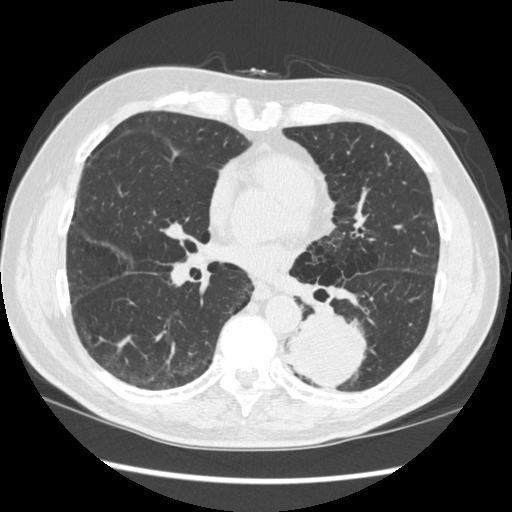
Low-dose screening chest CT, one axial slice; position 153 of 348 along the scan axis; reconstruction kernel STANDARD; 120 kVp; lung window (W 1500 / L -600 HU); 1.25 mm slice thickness; 512 × 512 image matrix, field of view 360 × 360 mm.
Outlined on this slice (outlined manually by an expert reader):
- lesion 1 (tumor, lower lobe of left lung): bounding box <286,314,366,390> (left, top, right, bottom; pixels)